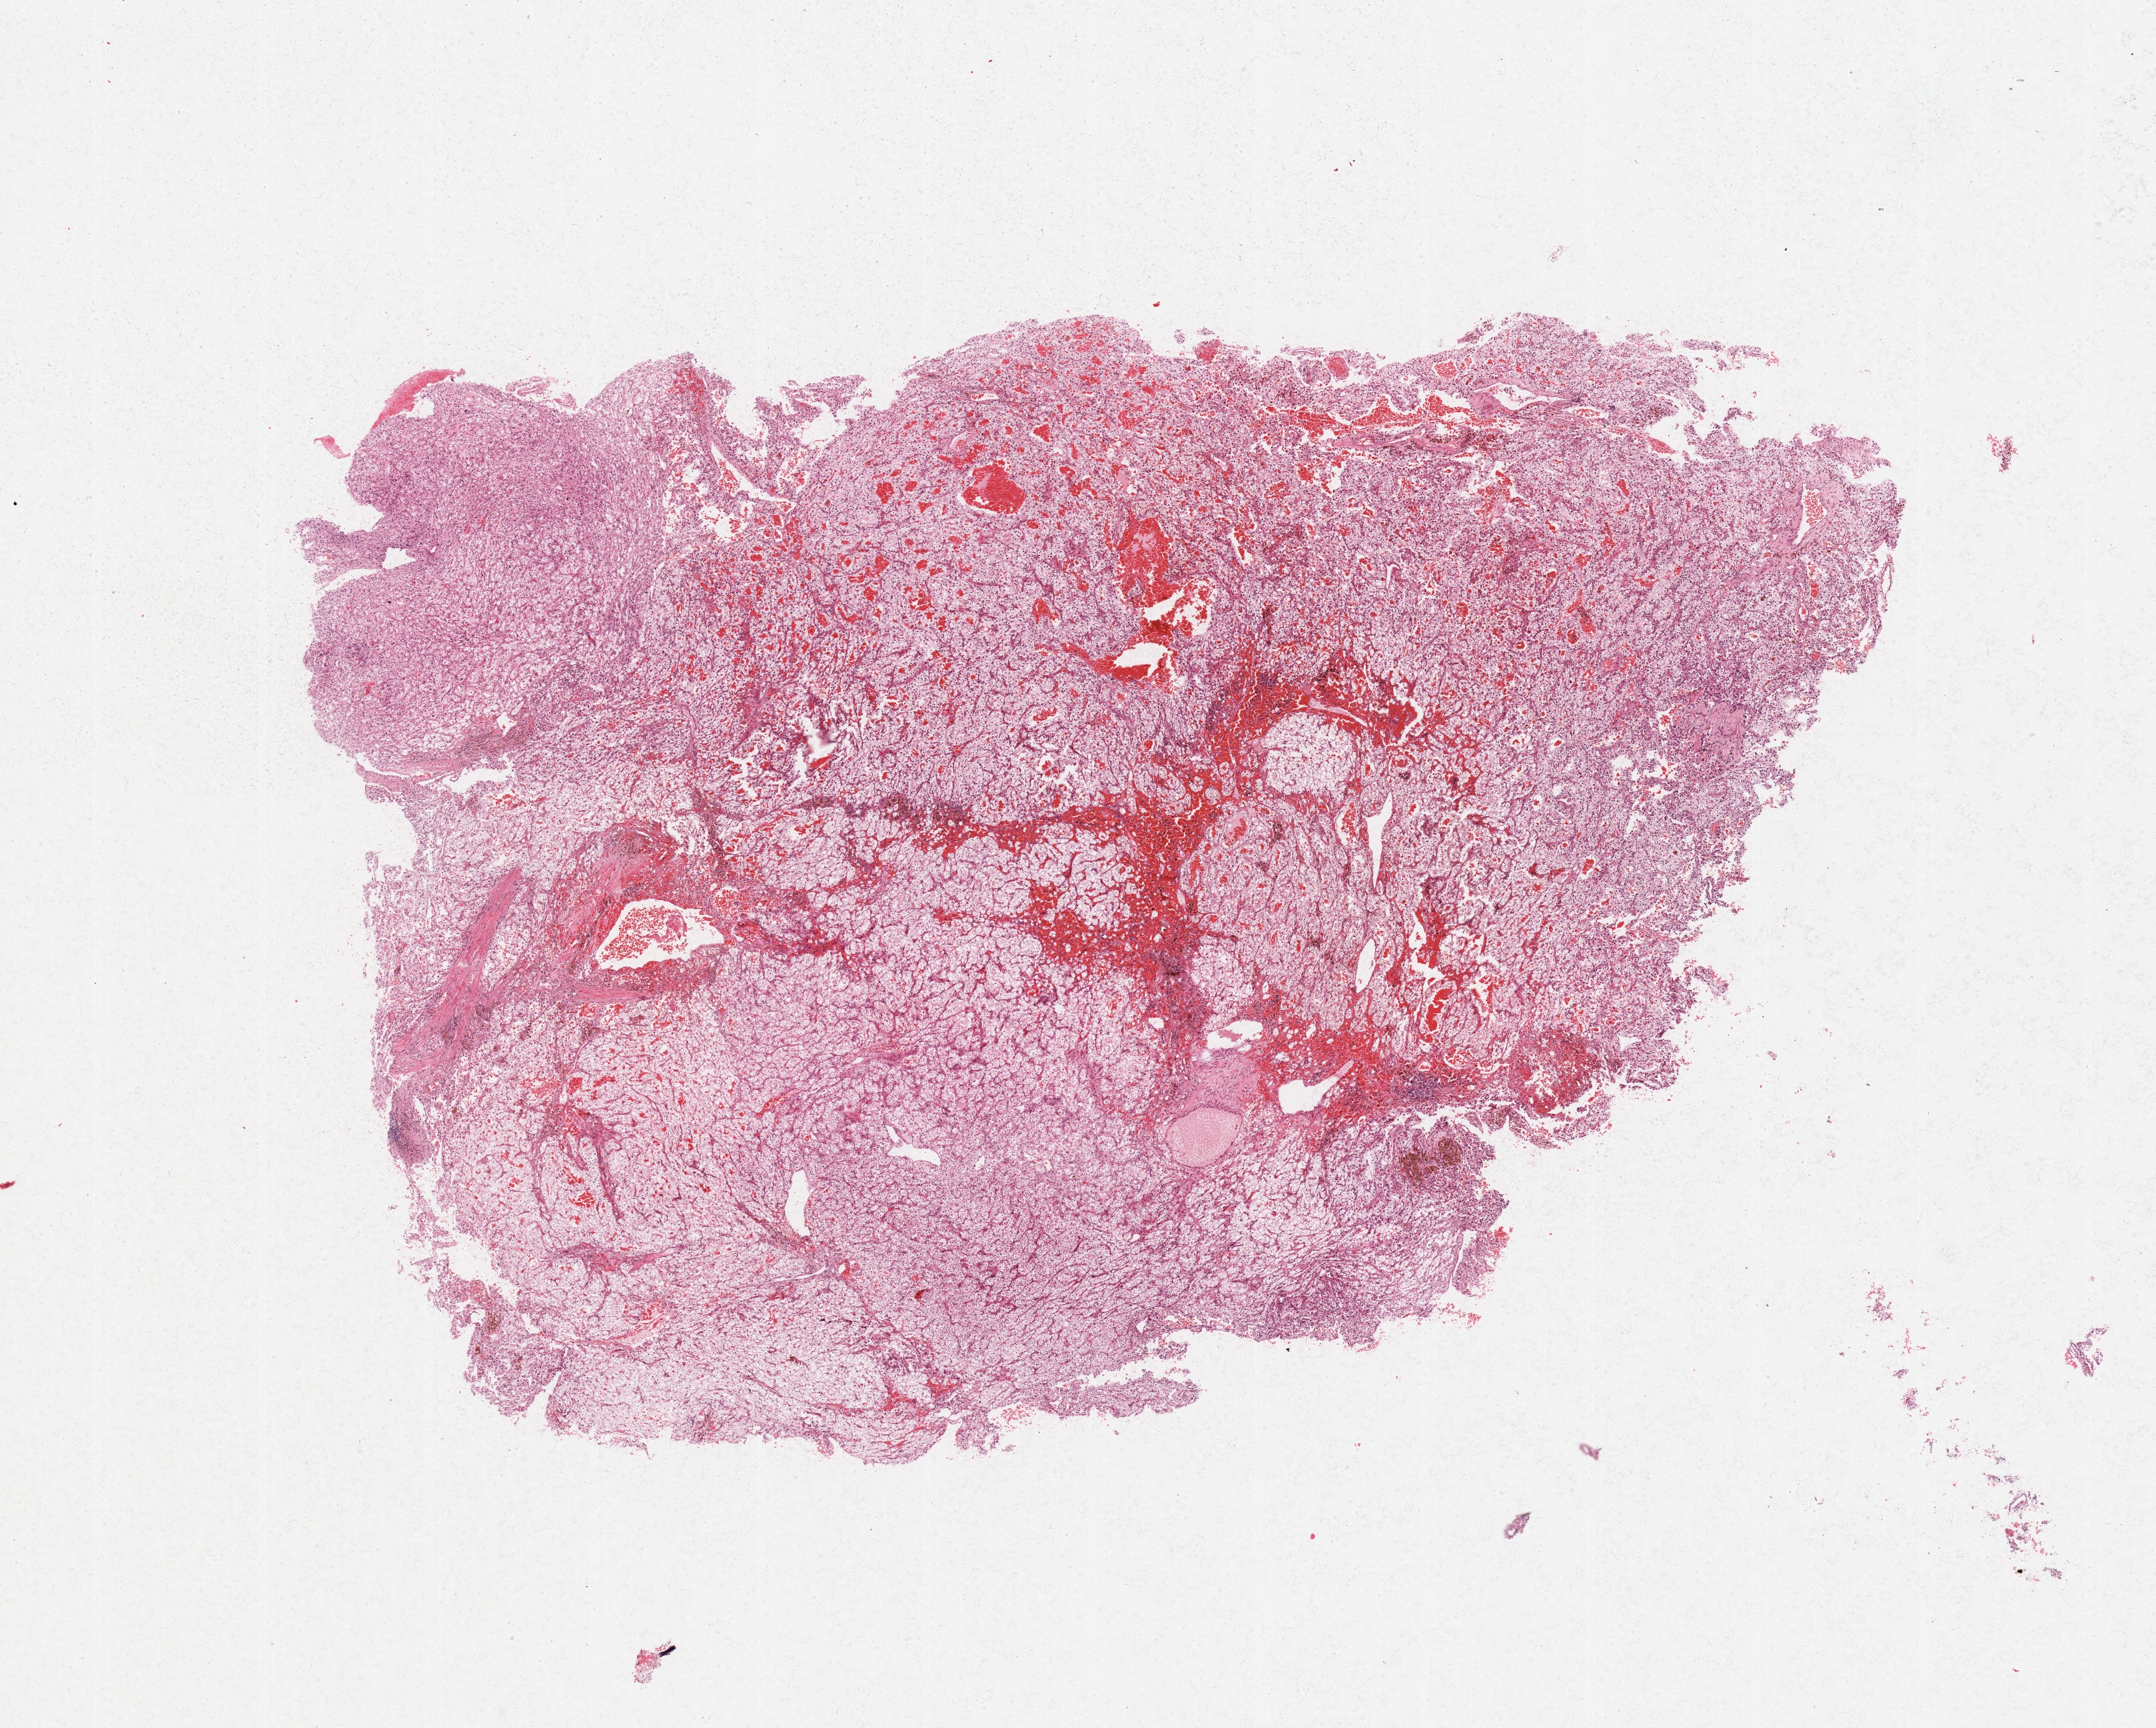
H&E whole-slide image, a low-resolution overview of the entire scanned area, about 12.8 x 10.3 mm (from a 20x scan), tumour tissue sample, sampled site: kidney. Patient: male, age 76 years. Histologic grade: G2 (moderately differentiated). Slide review estimates, as recorded: tumour nuclei 90%, necrosis 0%.
AJCC pathologic stage: I. Primary tumour site (as recorded): upper pole. Histologic diagnosis: Renal cell carcinoma, NOS.